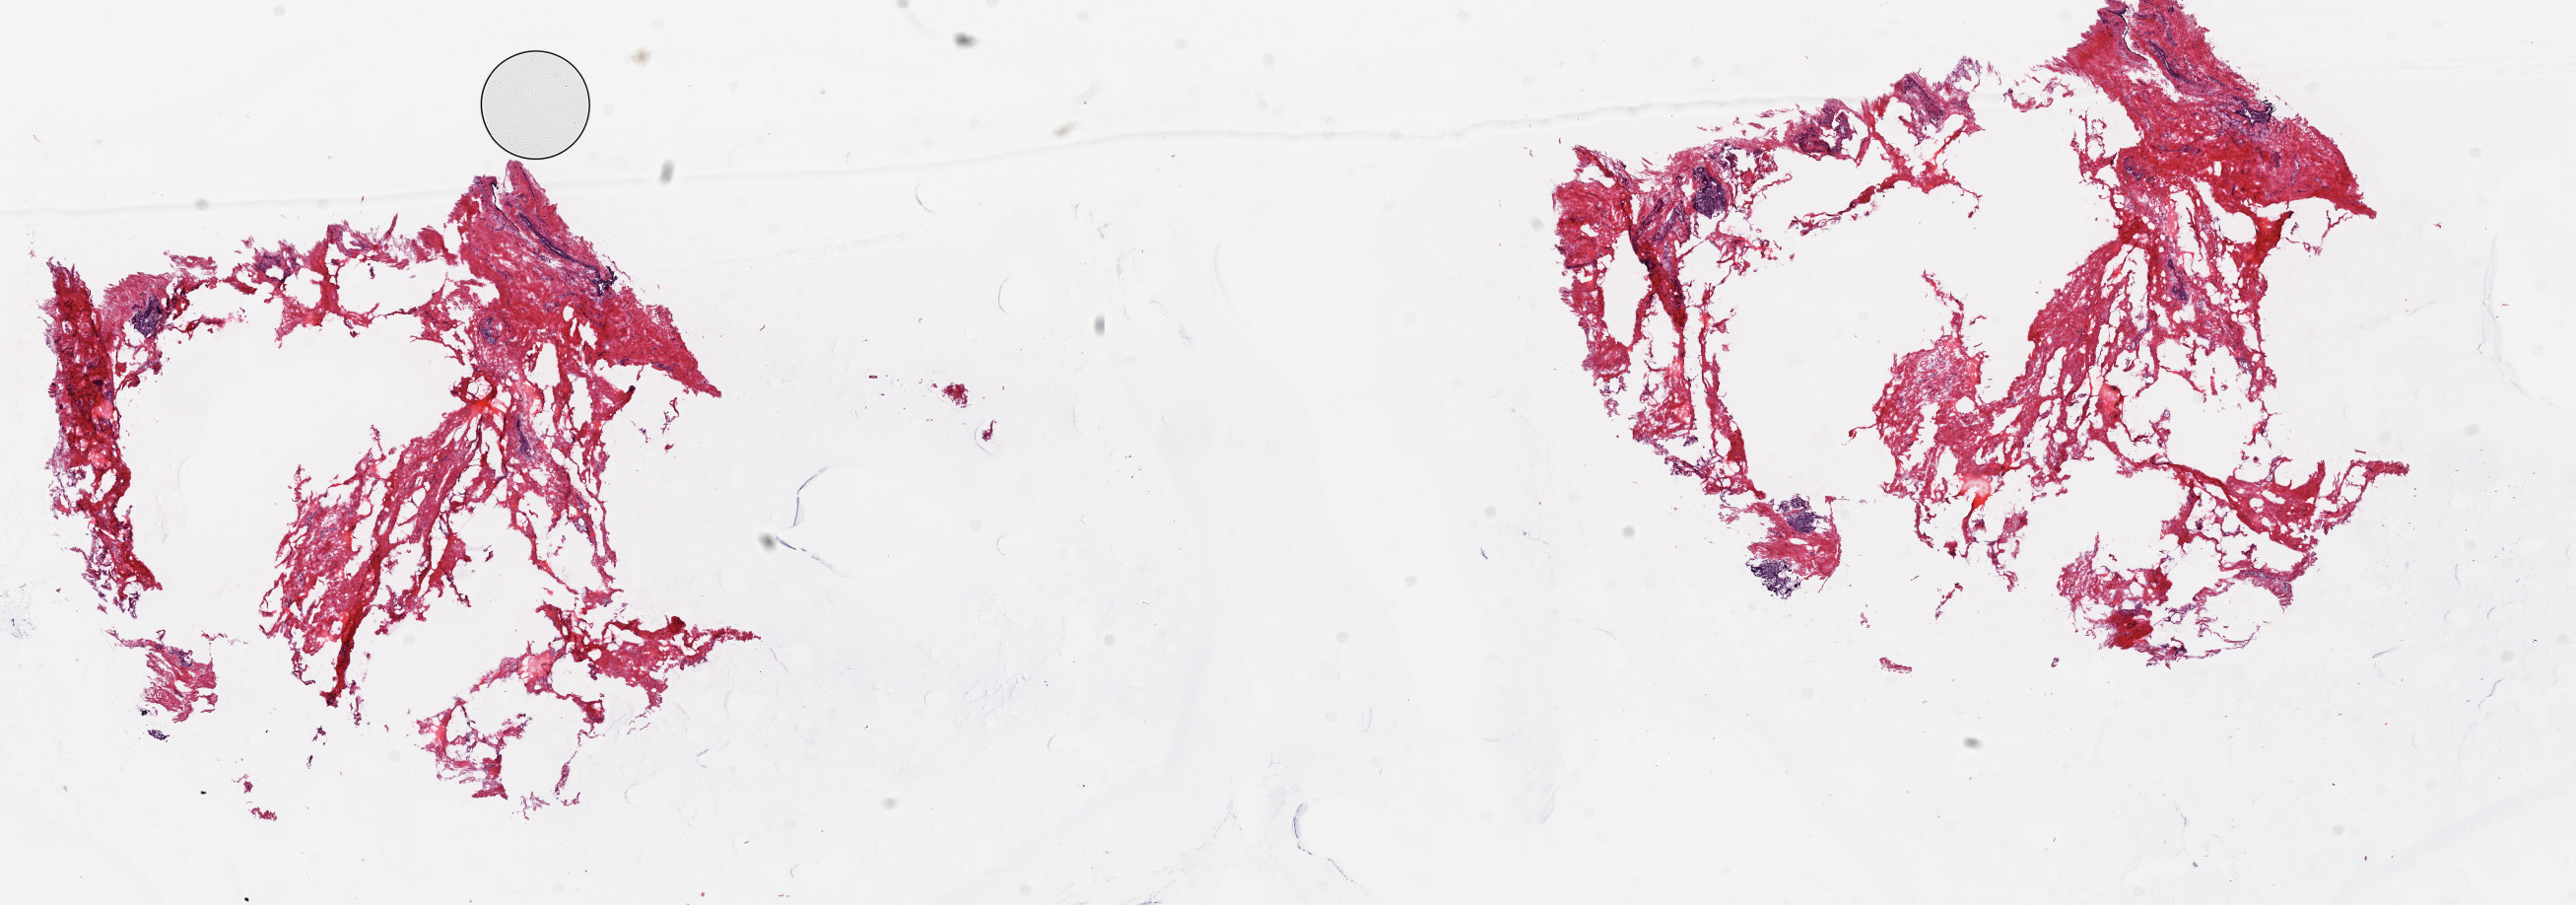
Digitized H&E tissue section (whole slide), a low-resolution overview of the entire scanned area, about 20.7 x 7.3 mm (from a 20x scan); frozen section from the top of the tissue portion; solid tissue normal (non-tumour tissue) sample from the breast. Patient: female, age at initial diagnosis 58 years. Pathologist review of this section (percent, as recorded): tumour cells 0%, tumour nuclei 0%, normal cells 15%, stromal cells 85%, necrosis 0%. Inflammatory infiltration, as recorded: lymphocyte infiltration 1%, monocyte infiltration 0%, neutrophil infiltration 0%.
This section: solid tissue normal sample (biorepository sample class). Patient diagnosis: Infiltrating duct carcinoma, NOS.